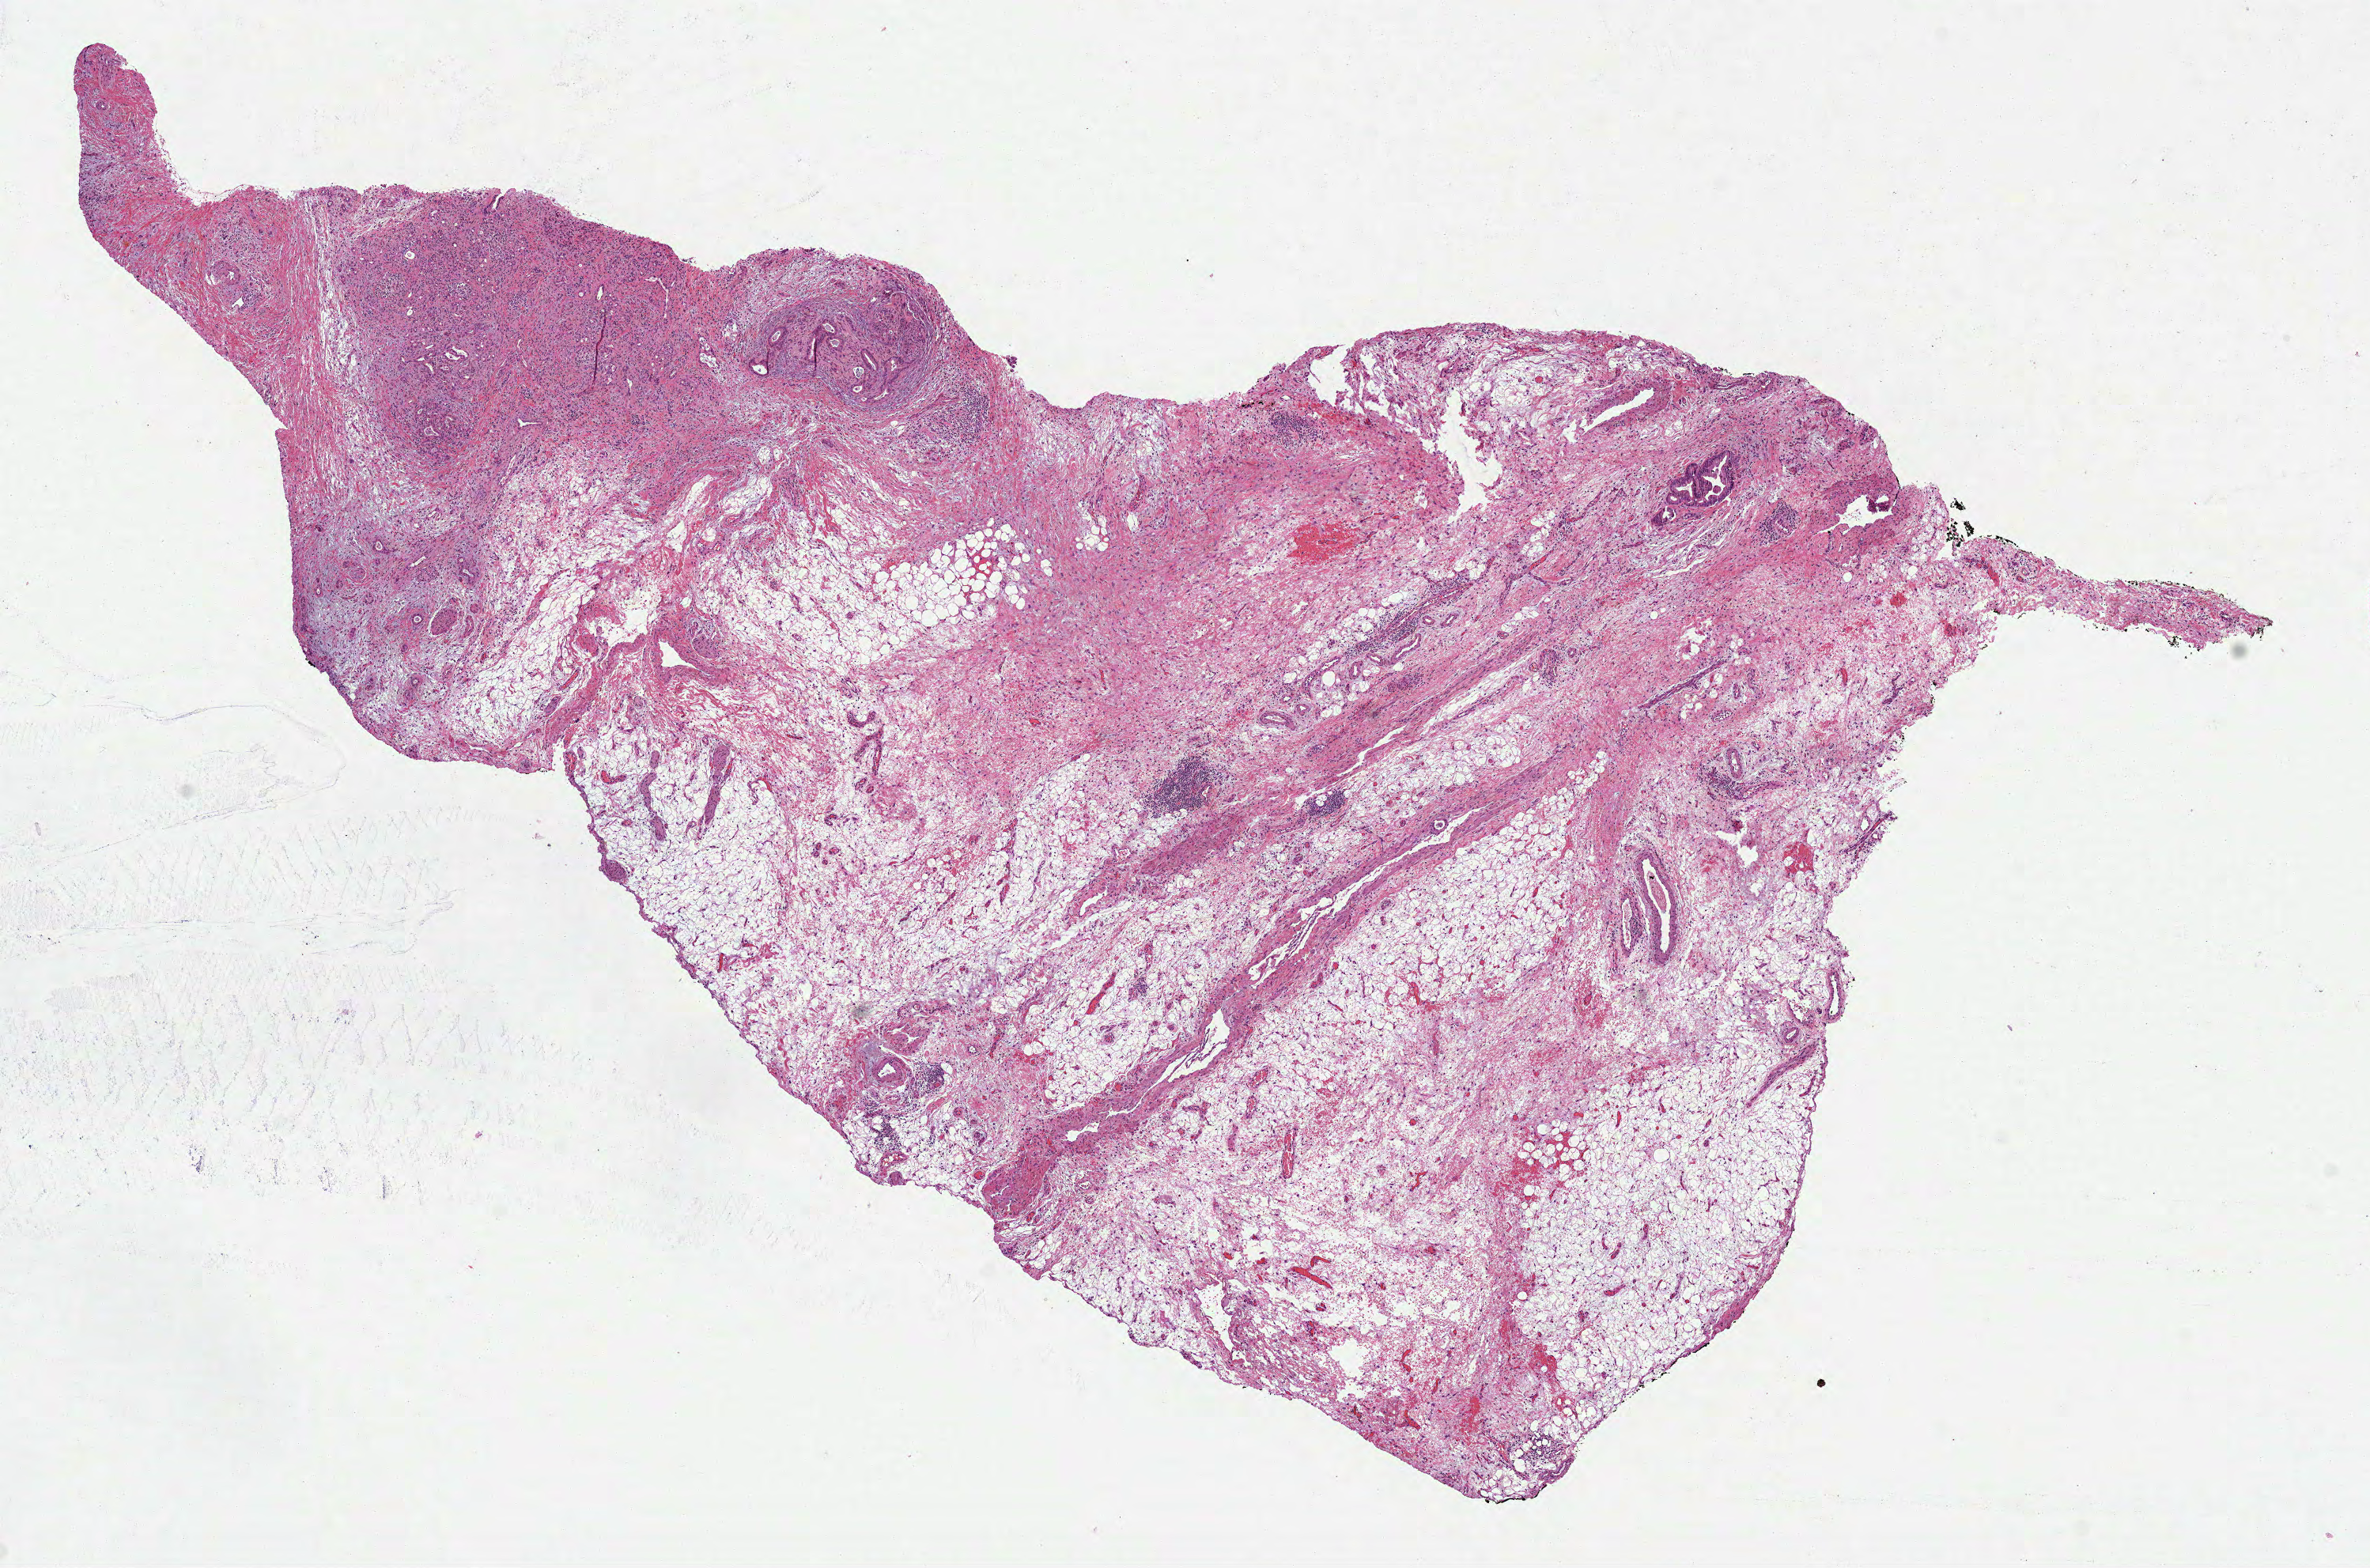
Whole-slide histology image, H&E-stained — low-resolution overview of the scanned area, about 12.1 x 8.0 mm; formalin-fixed paraffin-embedded (FFPE) diagnostic section; sample: primary tumour, pancreas. Female, age 68 years at initial diagnosis.
Histologic diagnosis: Infiltrating duct carcinoma, NOS (head of pancreas).